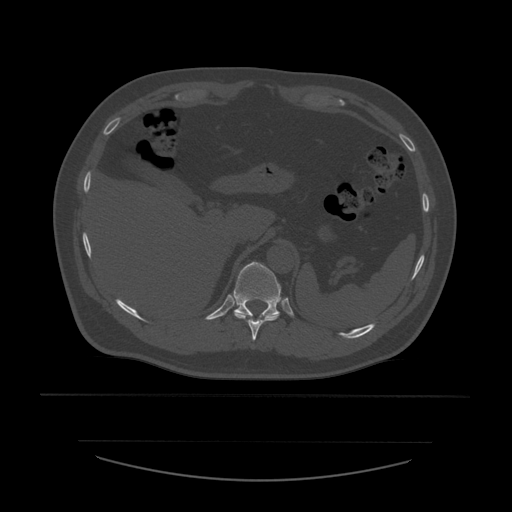
CT including the spine, one axial slice. Position 285 of 532 along the scan axis. 120 kVp. Bone window (W 1800 / L 400 HU). 1.25 mm slice thickness. 512 × 512 image matrix, field of view 441 × 441 mm. Patient age 44 years. From the clinical record (not read from this slice): primary cancer: soft tissue sarcoma.
Annotated regions visible in this slice (semi-automatically segmented with operator editing):
- T10 vertebra: bounding box [x1, y1, x2, y2] px = [234, 313, 280, 341]
- T11 vertebra: [234, 262, 281, 318]